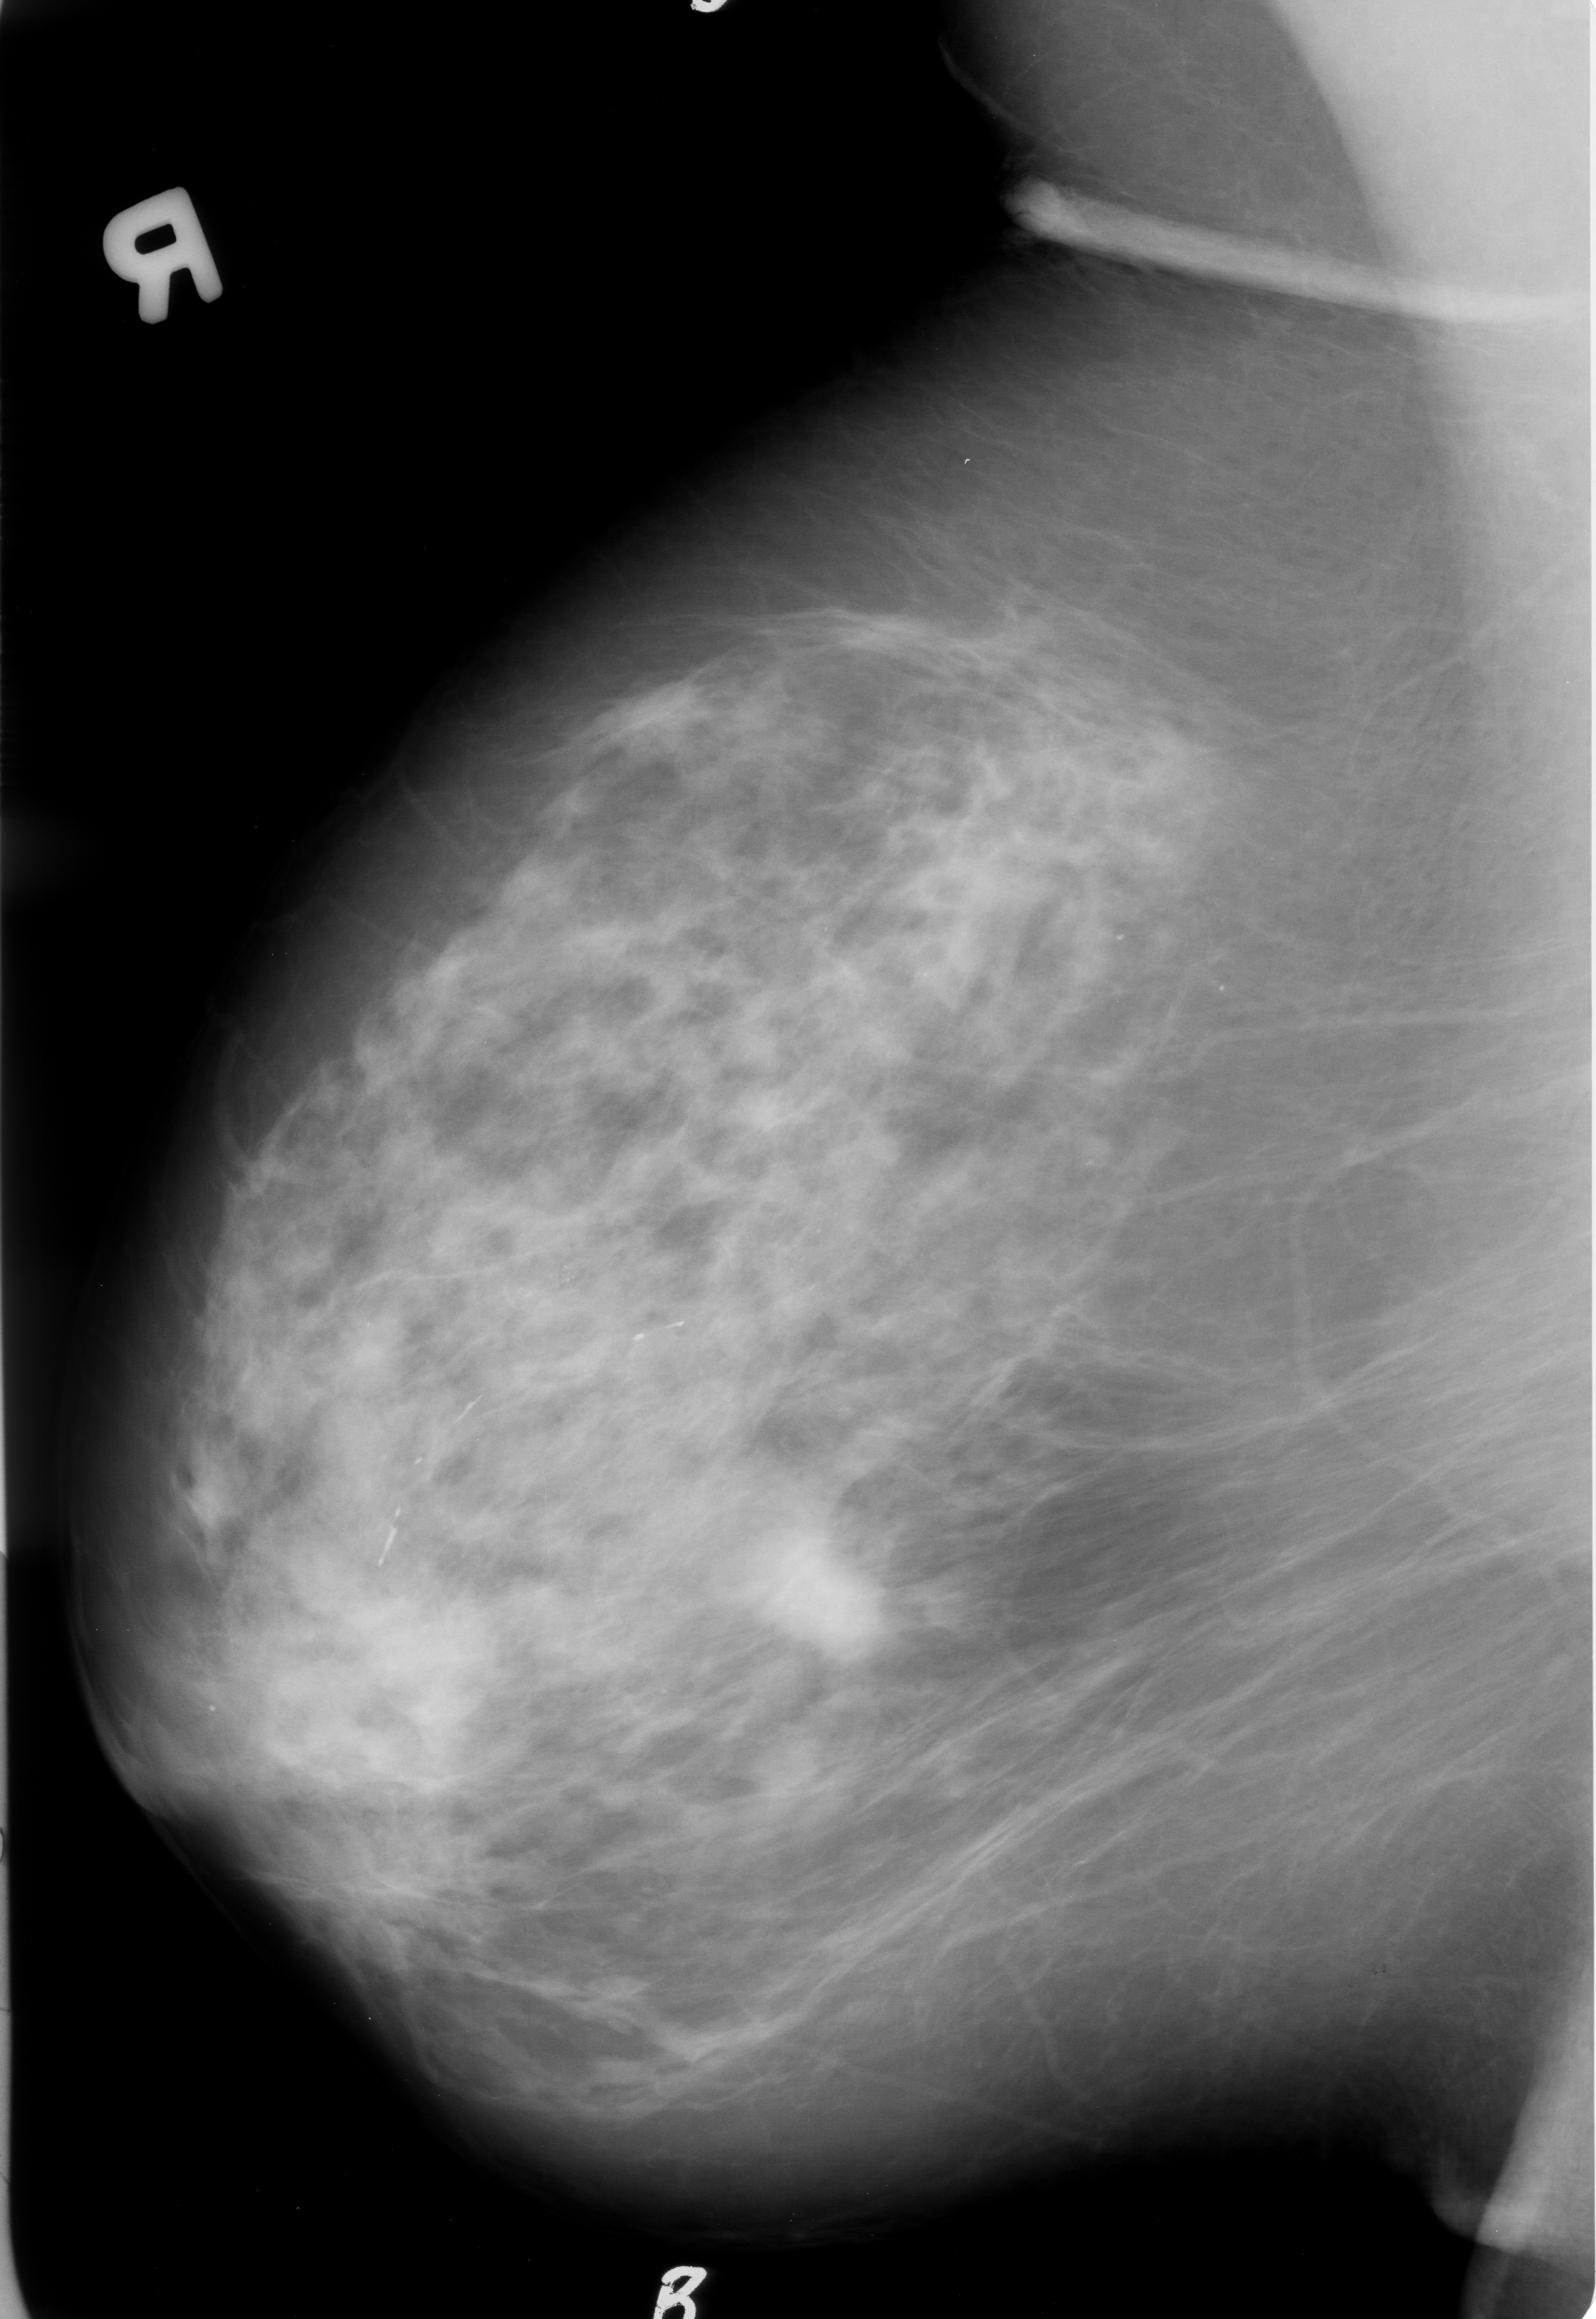
Mammogram (digitized film); right breast; mediolateral oblique (MLO) view; BI-RADS breast density category 3 (scale 1–4).
Marked findings (only marked abnormalities are described; nothing is implied about the rest of the image): mass, shape irregular / architectural distortion, margins obscured / spiculated; BI-RADS assessment category 5; subtlety rating 5 on a 1 (subtle) to 5 (obvious) scale; pathology result (as recorded, not read from the image): malignant.